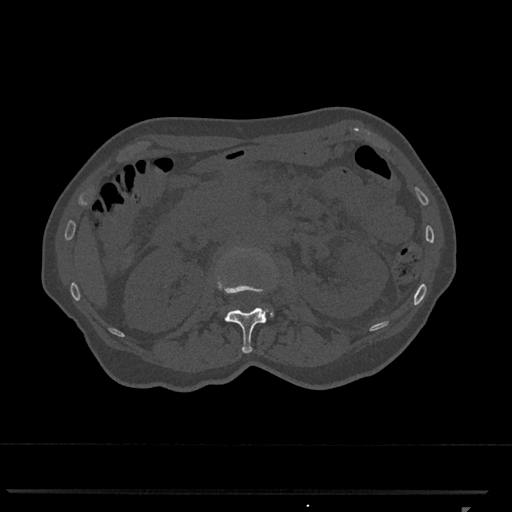
CT including the spine, one axial slice; position 383 of 793 along the scan axis; 120 kVp; bone window (W 1800 / L 400 HU); 512 × 512 image matrix, field of view 380 × 380 mm. Patient: female, 62 years. Case-level facts recorded for this patient, not image findings: primary cancer: renal.
Outlined on this slice (semi-automatic segmentation, software-assisted and operator-edited):
- L1 vertebra: bounding box [x1, y1, x2, y2] px = [217, 248, 268, 353]
- L2 vertebra: [270, 311, 274, 317]